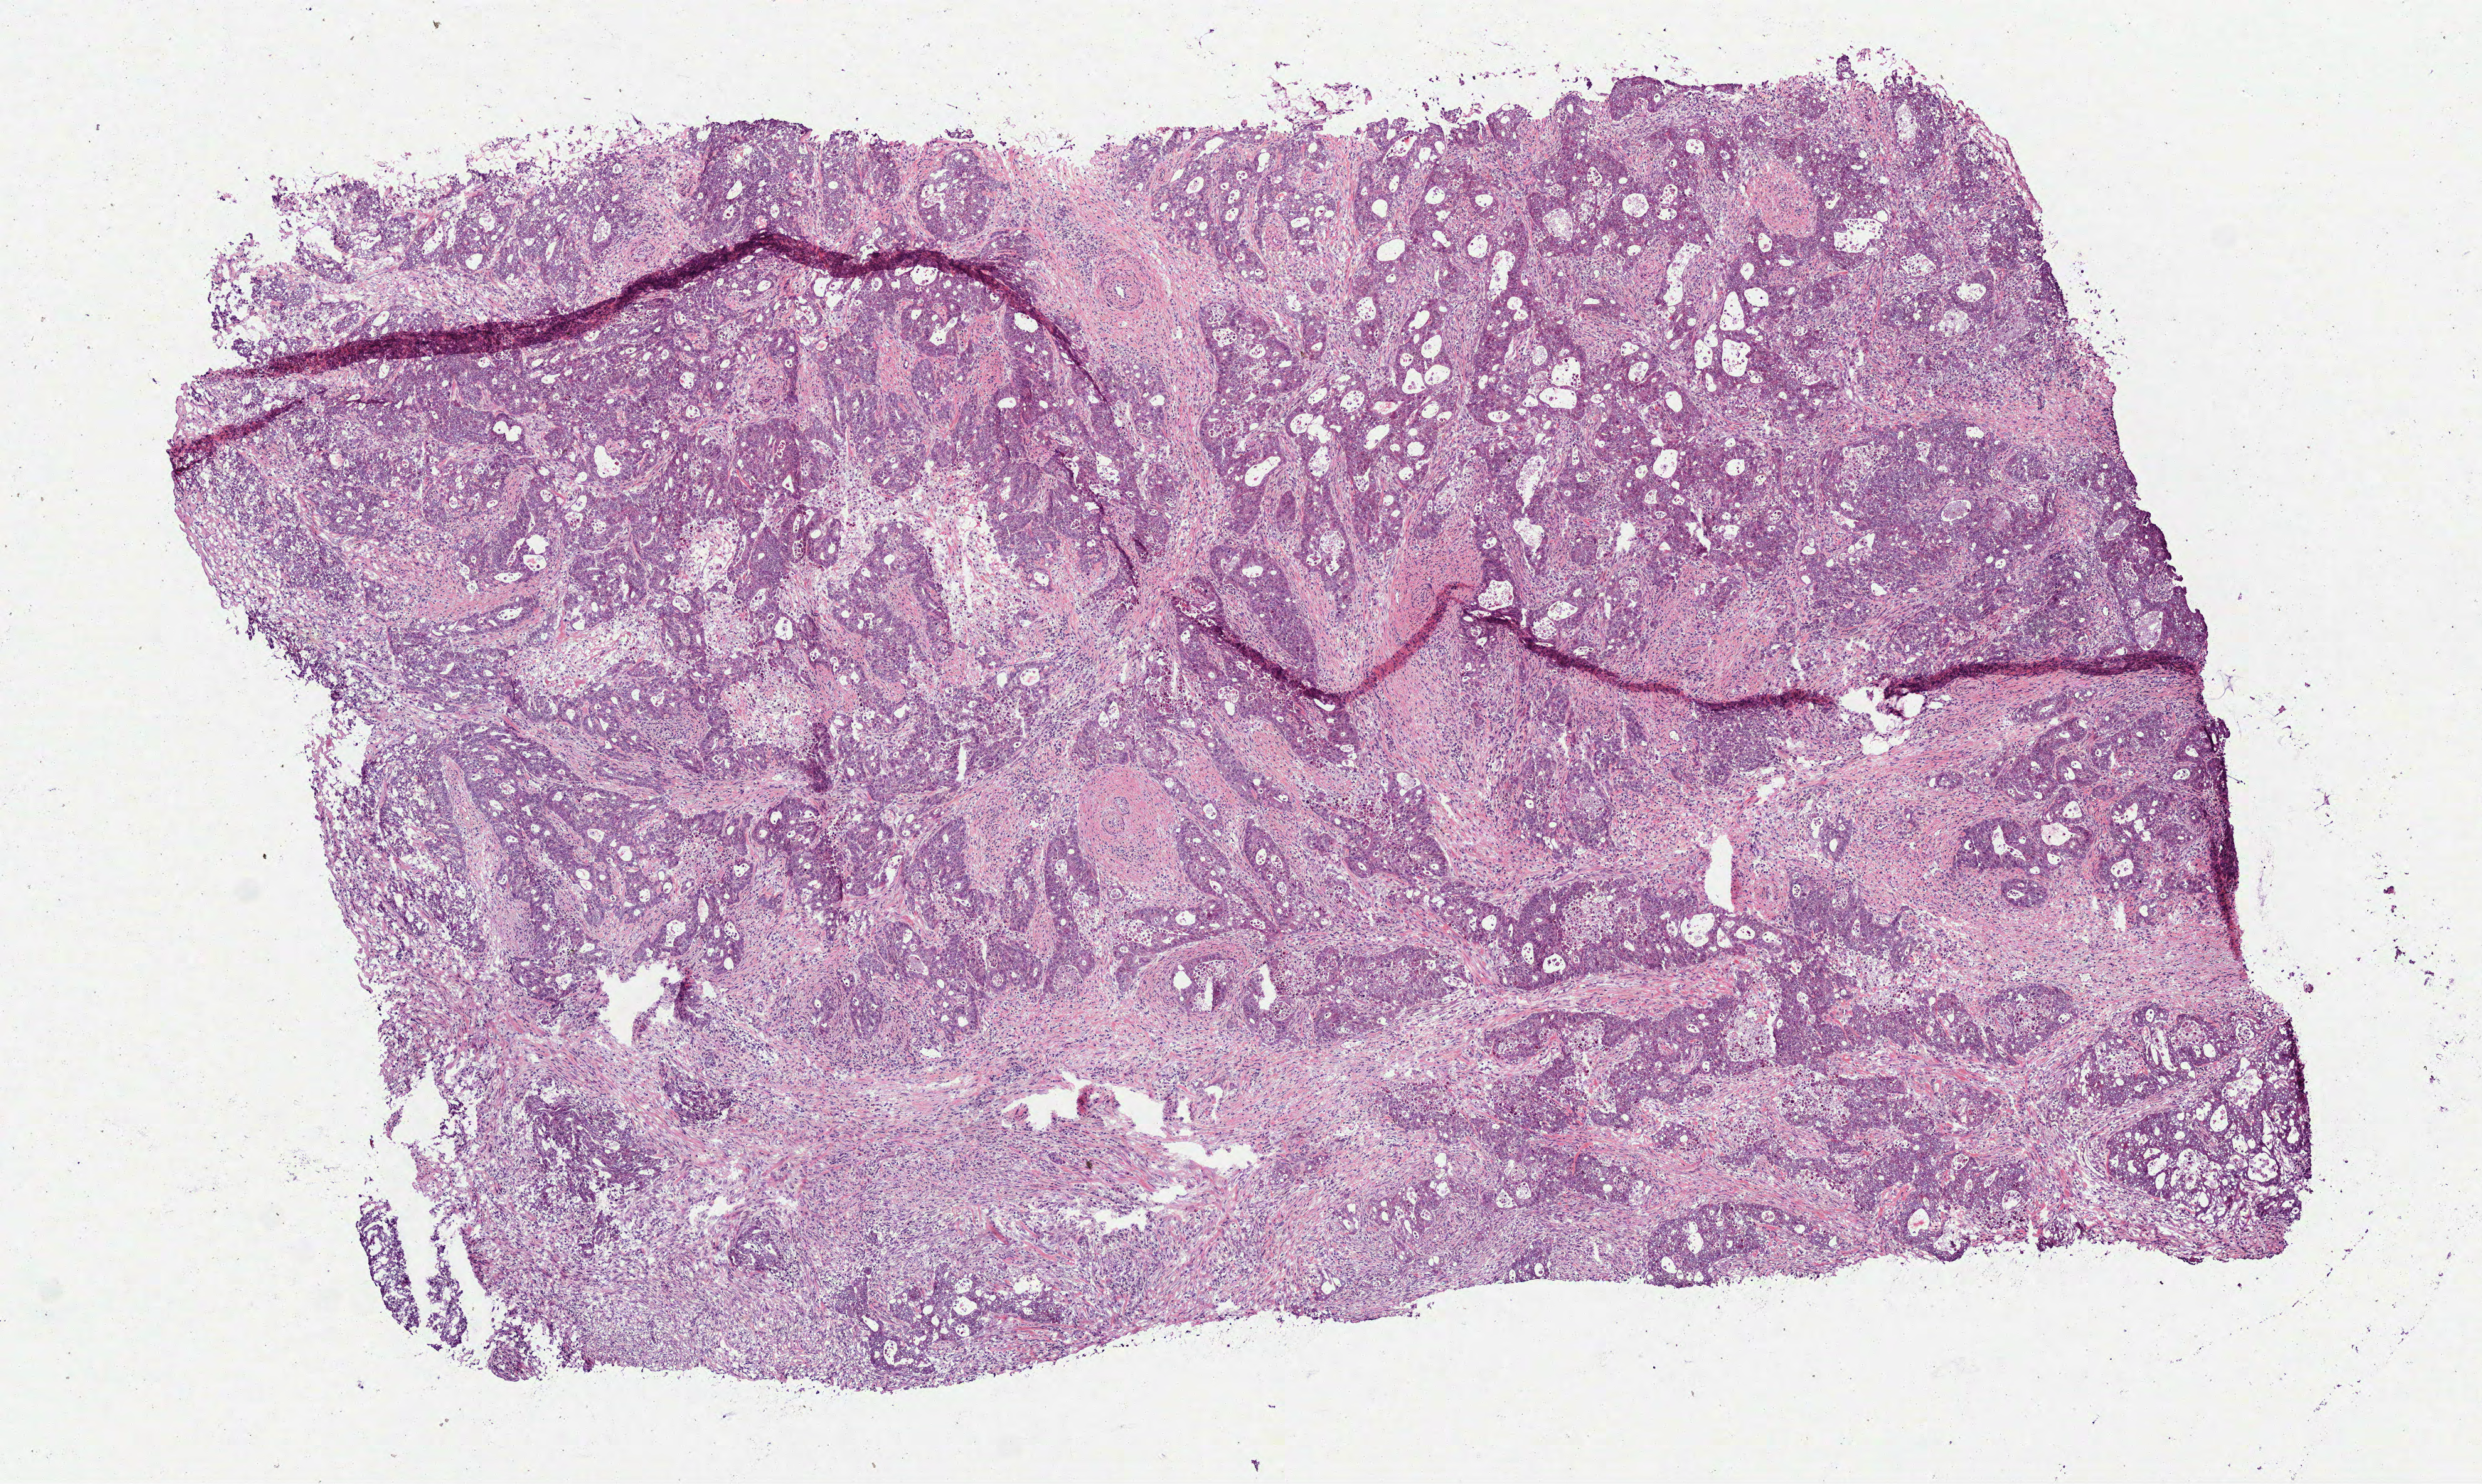
Digitized Hematoxylin and eosin (H&E) stained tissue section (whole slide), low-resolution overview of the scanned area, about 8.0 x 4.8 mm (acquisition: 40x scan); frozen section from the bottom of the tissue portion; primary tumour sample from the colon. Male, age 49 years at initial diagnosis. Slide review estimates, as recorded: tumour cells 99%, tumour nuclei 80%, normal cells 0%, stromal cells 0%, necrosis 1%. Inflammatory infiltration, as recorded: lymphocyte infiltration 5%, monocyte infiltration 2%, neutrophil infiltration 5%.
Diagnosis: Adenocarcinoma, NOS (splenic flexure of colon). AJCC pathologic stage: IIA. Lymph nodes positive (case pathology): 0 of 13 examined.